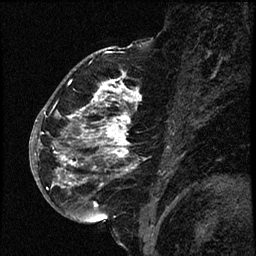
Breast MRI (dynamic contrast-enhanced), one sagittal slice. Position 34 of 66 along the scan axis. Dynamic contrast-enhanced study with each time point stored as its own series, time point 2 of 3 at this slice position (early post-contrast, ordered by acquisition time). 1.5 T. TE 4.2 ms, TR 17.6 ms. 256 × 256 image matrix, field of view 200 × 200 mm. Female patient. Case-level facts recorded for this patient, not image findings: setting: breast cancer imaged before/during neoadjuvant chemotherapy; receptor status: HER2-positive.
Structures marked on this image (semi-automatic segmentation, software-assisted and operator-edited):
- analysis volume of interest (the breast-tissue region the enhancement analysis was run in; not a lesion): bounding box [x1, y1, x2, y2] px = [52, 69, 151, 209]
- tumour enhancement mask (voxels above the 100 % enhancement threshold inside the analysis volume of interest): [56, 77, 140, 205]